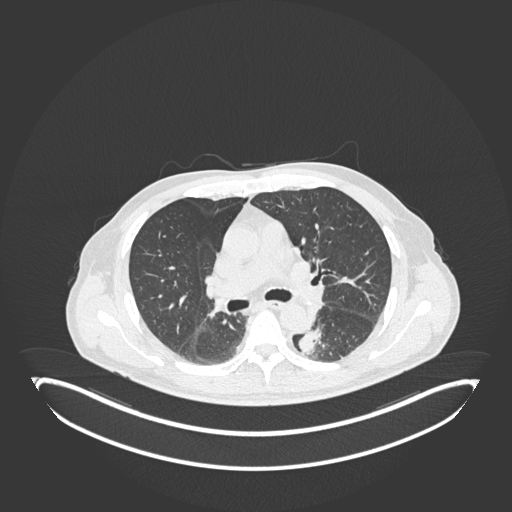
Chest CT, one axial slice. Slice 127 of 251 in the series (ordered by position). 120 kVp. Lung window (W 1500 / L -600 HU). 1 mm slice thickness. 512 × 512 image matrix, field of view 500 × 500 mm. Male patient, age 72 years. From the clinical record (not read from this slice): clinical TNM (as recorded): T2b N0 M1.
Outlined on this slice (bounding box drawn by a radiologist):
- lung tumour (recorded histology: adenocarcinoma): box from (x=294, y=325) to (x=328, y=360) px